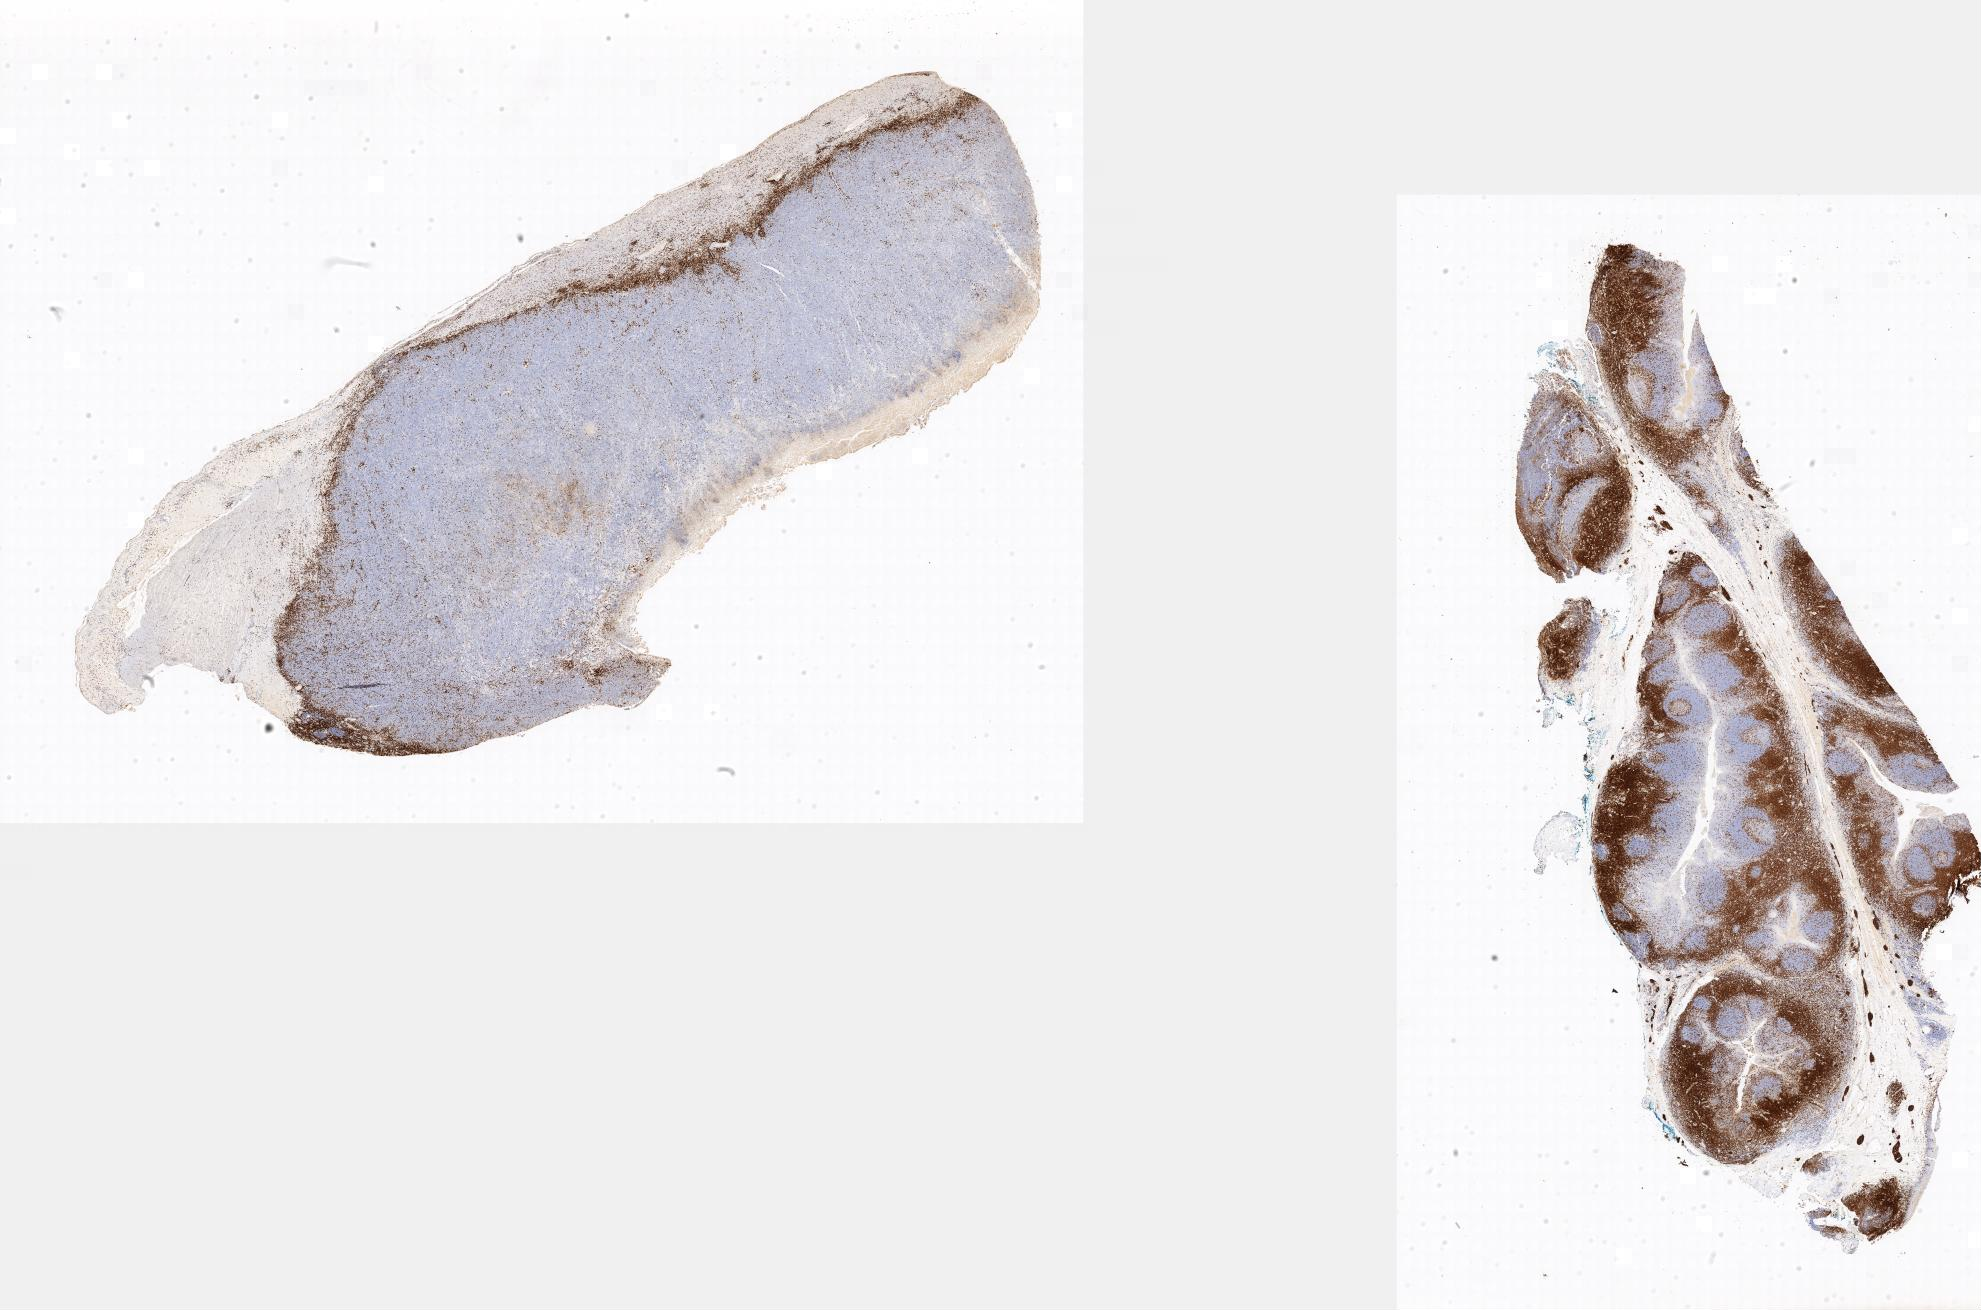
IHC for CD3, whole-slide image — a low-resolution overview of the entire scanned area; specimen: tumor tissue; site: small intestine. Male, age 3 years at initial diagnosis.
Diagnosis: Burkitt lymphoma, NOS.